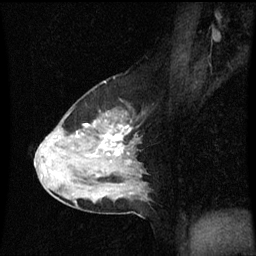
Breast MRI (dynamic contrast-enhanced), one sagittal slice. Slice 39 of 60 in the series (ordered by position). Dynamic contrast-enhanced series, image 2 of 3 at this slice position (ordered by acquisition). 1.5 T. TE 4.2 ms, TR 8.9 ms. 2 mm slice thickness. 256 × 256 image matrix. Patient: female, 50 years. From the clinical record (not read from this slice): setting: breast cancer imaged before/during neoadjuvant chemotherapy; receptor status: HR-positive, HER2-negative.
Structures marked on this image (semi-automatically segmented with operator editing):
- analysis volume of interest (the breast-tissue region the enhancement analysis was run in; not a lesion): box from (x=36, y=108) to (x=147, y=209) px
- tumour enhancement mask (voxels above the 70 % enhancement threshold inside the analysis volume of interest): (x=88, y=124)–(x=123, y=155)